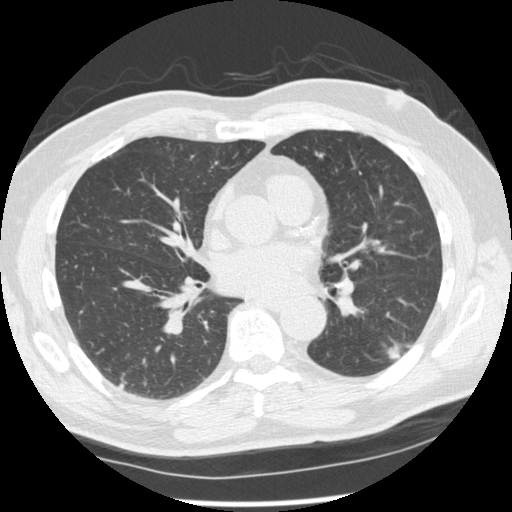
Chest CT (low-dose screening protocol), one axial image, second annual screen, lung window (W 1500 / L -600 HU), 1.25 mm slice thickness, standard (soft-tissue) reconstruction kernel (STANDARD), slice 127 of 227 in the series. Male, age 74 years at enrolment.
Expert reader's lesion annotation, bounding box <365,311,426,369> (left, top, right, bottom; pixels). The screening reader recorded 7 non-calcified nodules or masses ≥4 mm on this exam; which of them this box marks is not recorded. Official screen result: positive, other. Lung cancer was diagnosed 43 days after this screen: squamous cell carcinoma, NOS, left lower lobe, well differentiated (G1), stage IA (AJCC 6th edition), 28 mm at pathology.